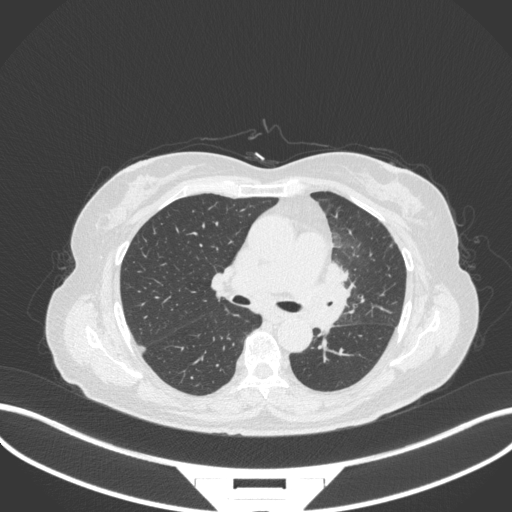
Chest CT, one axial slice. Slice 199 of 382 in the series (ordered by position). Lung window (W 1500 / L -600 HU). 512 × 512 image matrix, field of view 400 × 400 mm. Patient: female, 64 years. From the clinical record (not read from this slice): clinical TNM (as recorded): T2a N2 M0.
Outlined on this slice (bounding box drawn by a radiologist):
- lung tumour (recorded histology: adenocarcinoma): box from (x=315, y=259) to (x=357, y=336) px